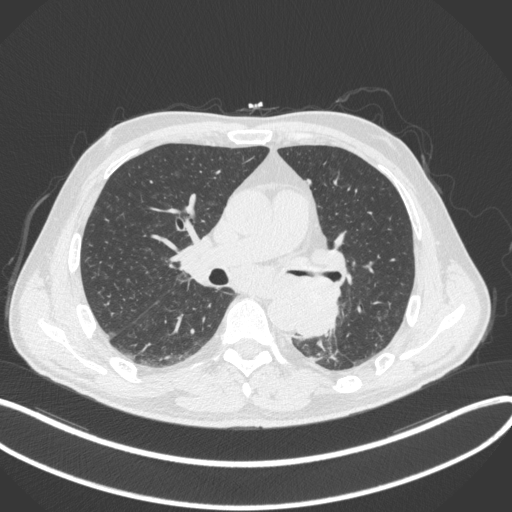
Chest CT, one axial slice; slice 192 of 328 in the series (ordered by position); reconstruction kernel B31f; 120 kVp; lung window (W 1500 / L -600 HU); 1 mm slice thickness; 512 × 512 image matrix, field of view 400 × 400 mm. Patient: male, 59 years. Case-level facts recorded for this patient, not image findings: clinical TNM (as recorded): T2a N2 M0.
Annotated regions visible in this slice (bounding box drawn by a radiologist):
- lung tumour (recorded histology: squamous cell carcinoma): bounding box (x1, y1, x2, y2) in pixels: (290, 287, 339, 341)